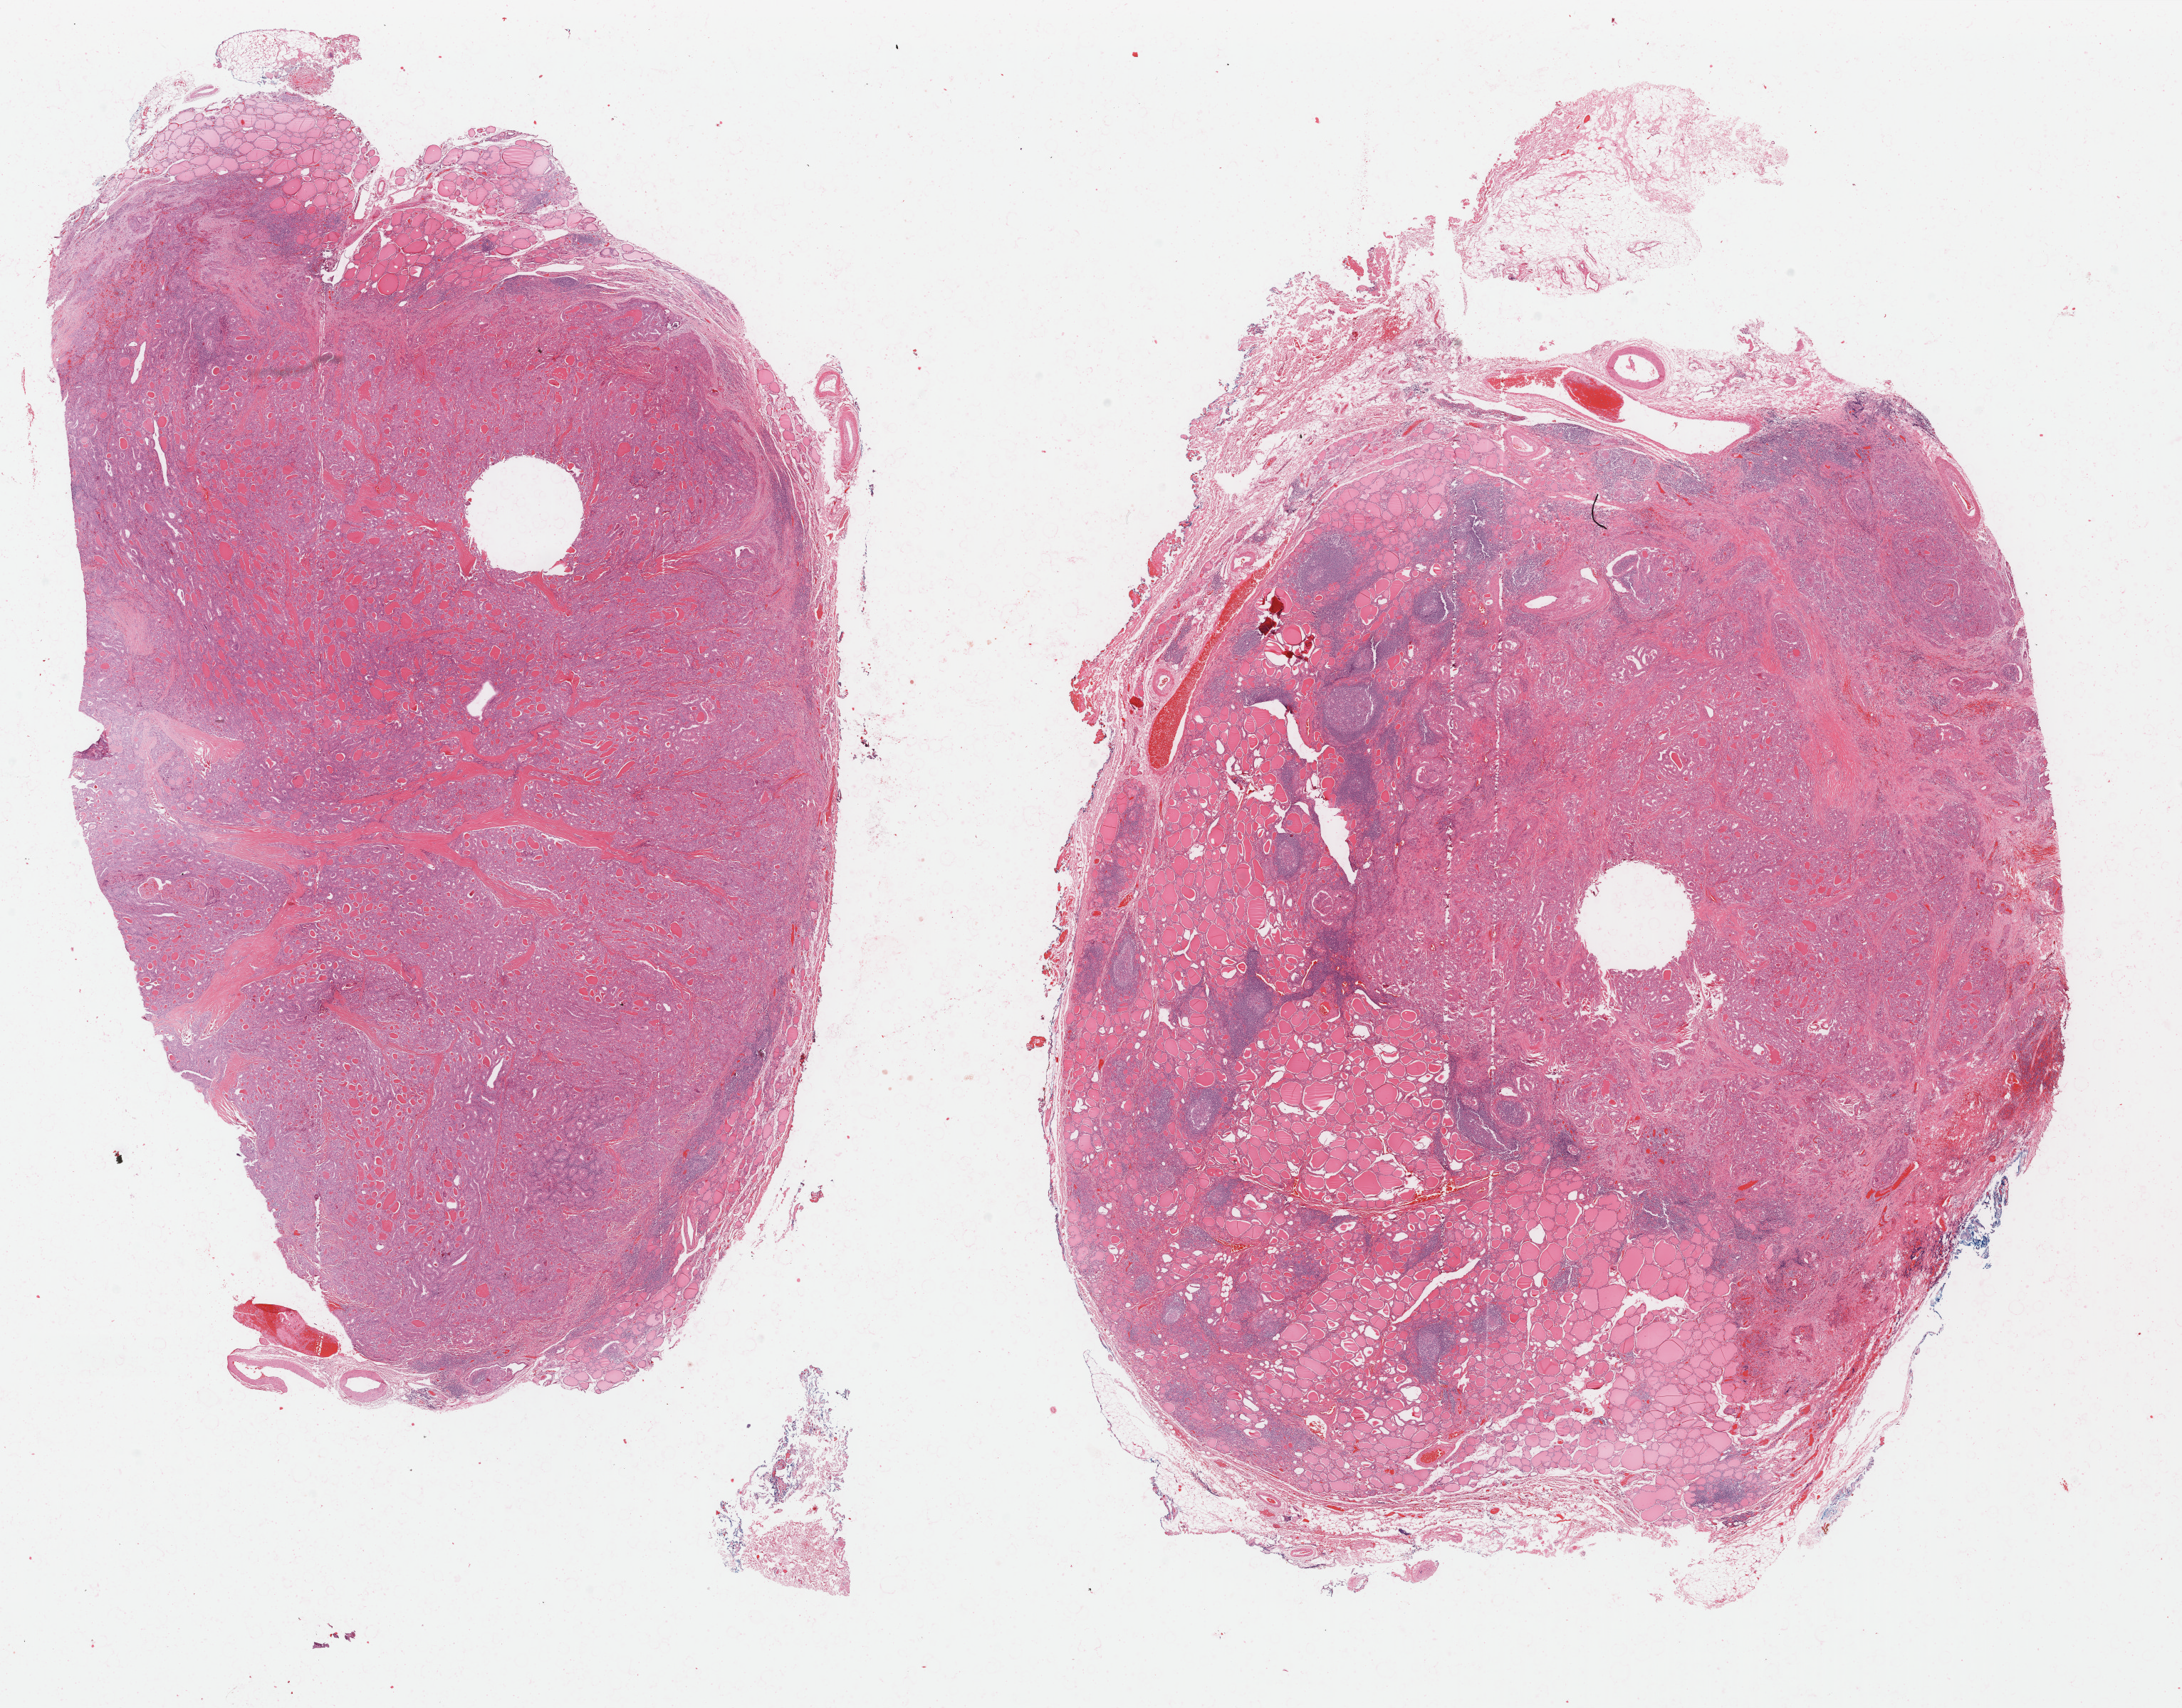
Whole-slide histology image, H&E, whole scanned area (about 24.3 x 19.0 mm, acquisition: 40x scan) shown as a low-resolution overview. Formalin-fixed paraffin-embedded (FFPE) diagnostic section. Thyroid, primary tumour sample. Patient: male, age at initial diagnosis 37 years.
Diagnosis: Papillary carcinoma, follicular variant (thyroid gland). AJCC pathologic stage: I (6th edition). Laterality: bilateral.